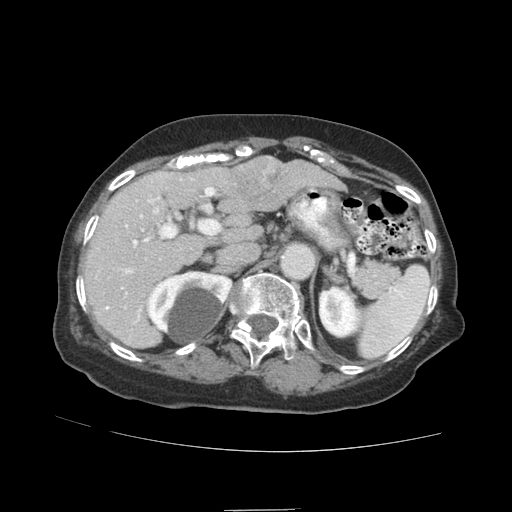
Contrast-enhanced abdominal CT (liver protocol), one axial slice; slice 55 of 89 in the series (ordered by position); reconstruction kernel STANDARD; 140 kVp; soft-tissue window (W 400 / L 40 HU); 2.5 mm slice thickness; 512 × 512 image matrix, field of view 360 × 360 mm. Case-level facts recorded for this patient, not image findings: diagnosis: hepatocellular carcinoma (patient treated with transarterial chemoembolisation; whether this scan precedes or follows treatment is not stated here); TNM stage (as recorded): Stage-II; Child-Pugh class: A; tumour differentiation: moderately differentiated; tumour nodularity: multinodular.
Outlined on this slice (semi-automatically segmented with operator editing):
- liver parenchyma outside the tumour (the mass and vessels are separate outlines, so this box may not span the whole liver): bounding box (x1, y1, x2, y2) in pixels: (84, 156, 334, 348)
- mass: (230, 156, 291, 212)
- liver vessels: (95, 175, 194, 342)